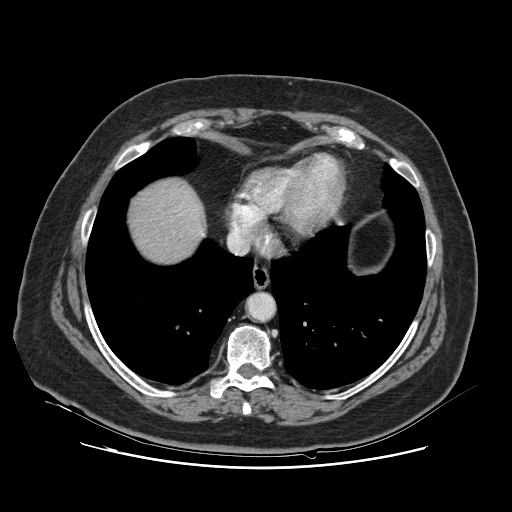
Contrast-enhanced abdominal CT, one axial slice; slice 116 of 132 in the series (ordered by position); 120 kVp; intravenous contrast given; soft-tissue window (W 400 / L 40 HU); 2.5 mm slice thickness; 512 × 512 image matrix, field of view 391 × 391 mm. Female patient, age 73 years. Case-level facts recorded for this patient, not image findings: diagnosis: colorectal cancer liver metastases, imaged before liver resection; multiple liver metastases: no; largest metastasis: 7 cm; disease in both lobes: no.
Structures marked on this image (manually delineated by an expert):
- liver: bounding box (x1, y1, x2, y2) in pixels: (129, 180, 200, 263)
- planned liver remnant (the part of the liver to remain after resection): (129, 180, 201, 262)